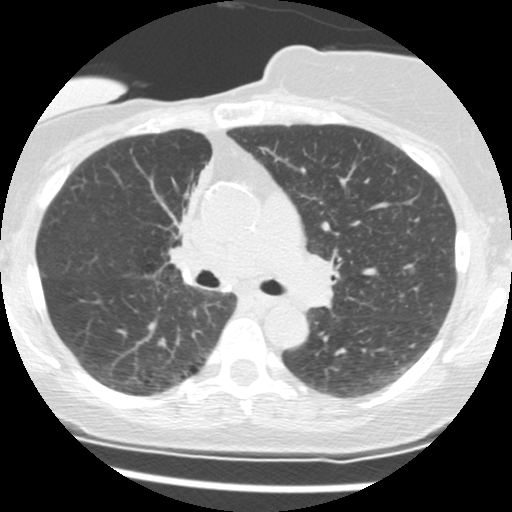
Chest CT (low-dose screening protocol), one axial image; second screening round (one year after baseline); lung window (W 1500 / L -600 HU). Female participant, aged 56 years at enrolment. Current smoker at enrolment.
Expert-annotated lung lesion, bounding box <152,160,207,255> (left, top, right, bottom; pixels). The screening reader recorded 2 non-calcified nodules or masses ≥4 mm on this exam (right middle lobe, right lower lobe); which of them this box marks is not recorded. Official screen result: positive, change unspecified: nodule(s) >= 4 mm or enlarging nodule(s), mass(es), or other non-specific abnormalities suspicious for lung cancer. Later outcome: lung cancer diagnosed 675 days after this screen (after the third annual screen) — adenocarcinoma, NOS, right upper lobe, stage IIIB (AJCC 6th edition), 8 mm at pathology.